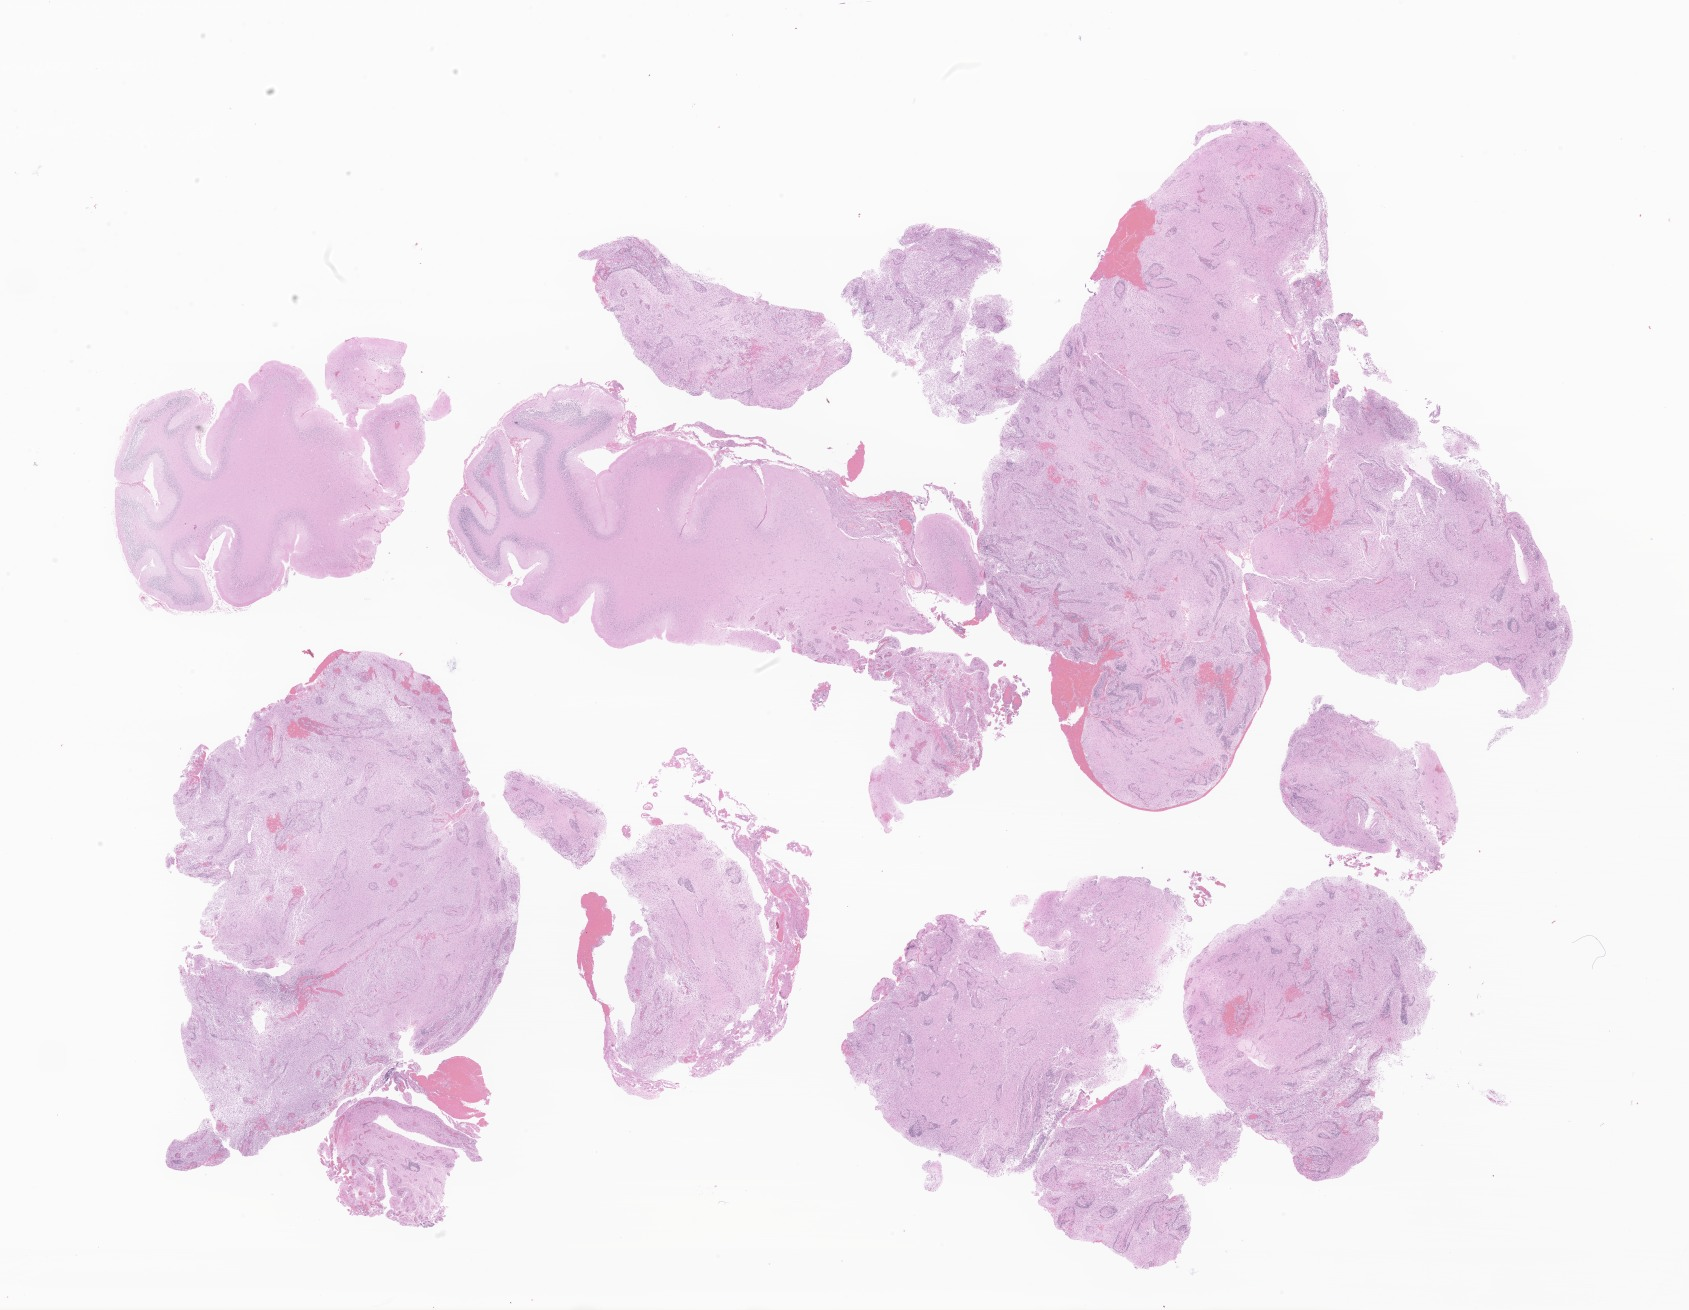
Whole-slide image, haematoxylin and eosin stain of tumor tissue from the brain — whole scanned area (about 28.5 x 22.1 mm) shown as a low-resolution overview. Formalin-fixed paraffin-embedded section. Patient: male, age 104 months (8 years 8 months).
• recorded diagnosis: Pilocytic astrocytoma